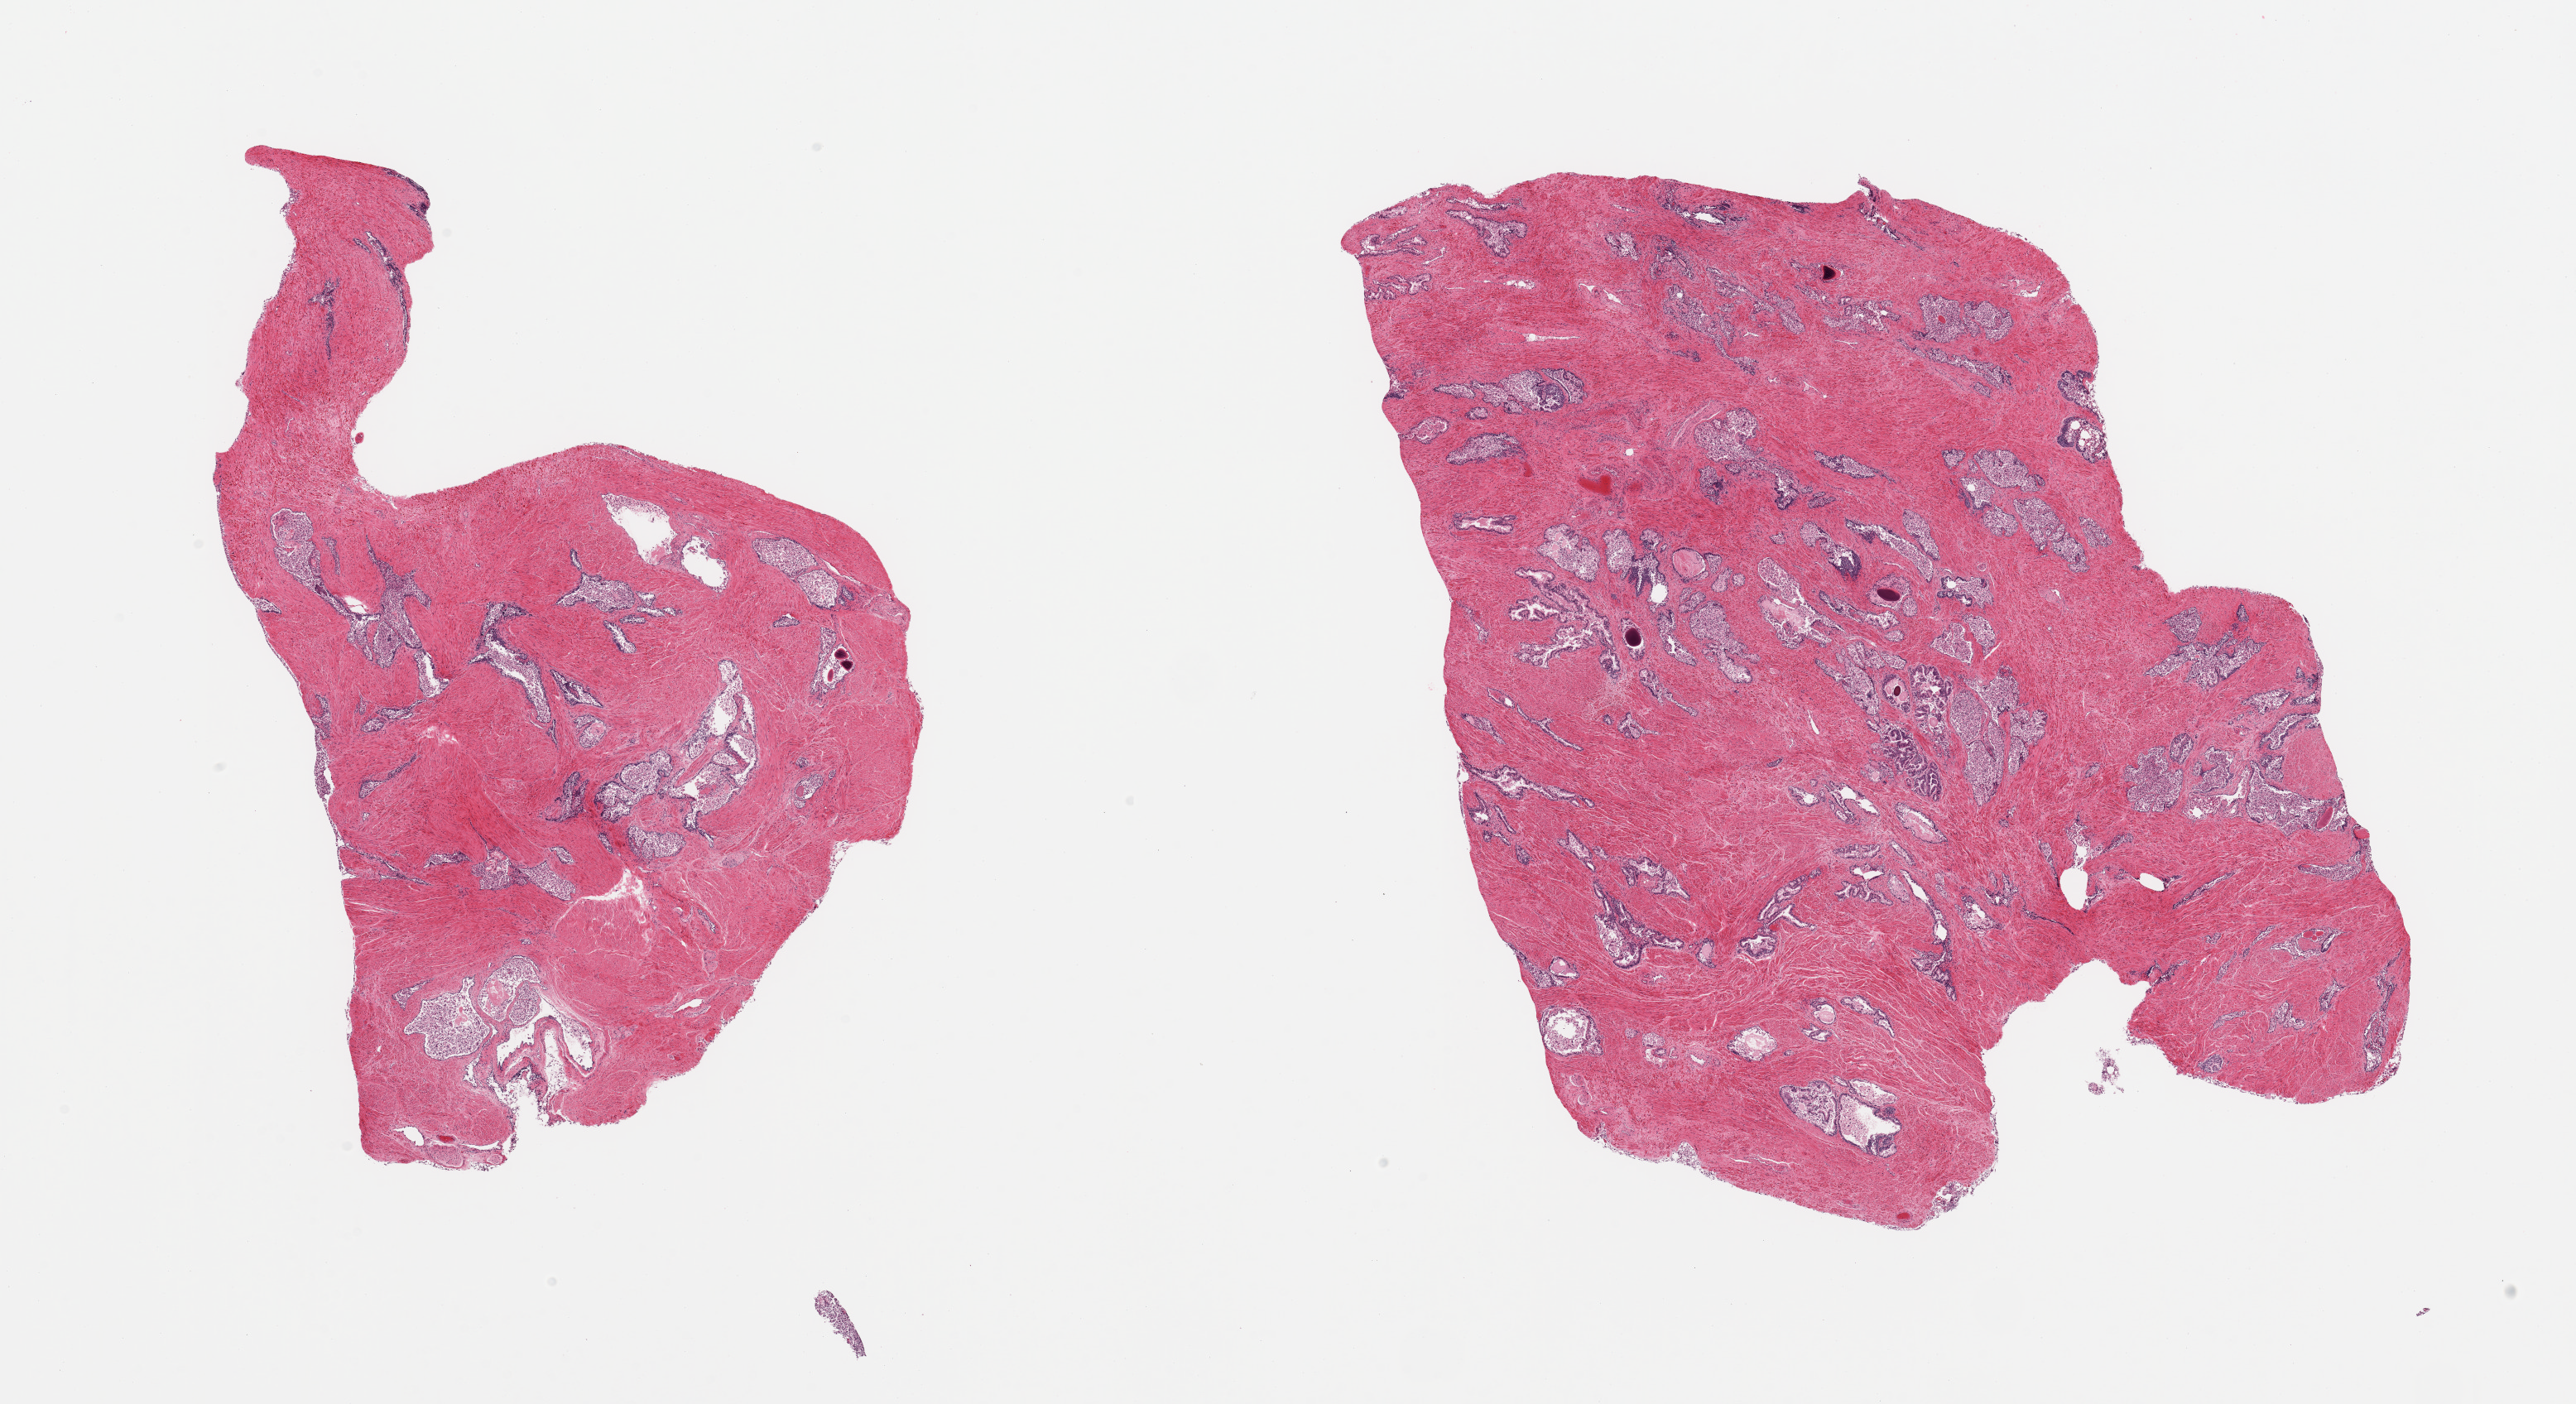
Whole-slide image, haematoxylin and eosin stain, low-resolution overview of the scanned area, about 24.6 x 13.4 mm (slide scanned at 20x); PAXgene-fixed, paraffin-embedded tissue; section of prostate (target tissue); donor tissue sample. Donor: male.
• review note (as recorded): 2 pieces; glands autolyzed, stroma intact